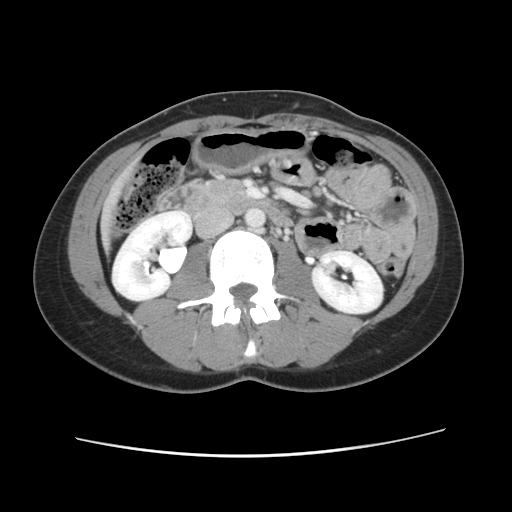
Contrast-enhanced abdominal CT, one axial slice. Position 22 of 134 along the scan axis. 120 kVp. Intravenous contrast given. Soft-tissue window (W 400 / L 40 HU). 512 × 512 image matrix, field of view 339 × 339 mm. Female patient, age 33 years. From the clinical record (not read from this slice): diagnosis: colorectal cancer liver metastases, imaged before liver resection; multiple liver metastases: yes; largest metastasis: 4.5 cm; chemotherapy before resection: no.
Structures marked on this image (expert manual segmentation):
- liver: bounding box <101,166,135,247> (left, top, right, bottom; pixels)